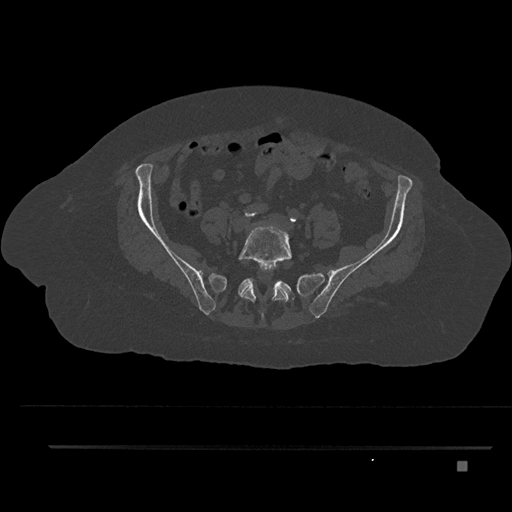
CT including the spine, one axial slice; slice 29 of 797 in the series (ordered by position); reconstruction kernel Br40s/3; 120 kVp; bone window (W 1800 / L 400 HU); 0.5 mm slice thickness; 512 × 512 image matrix, field of view 437 × 437 mm. Patient: female, 76 years. Case-level facts recorded for this patient, not image findings: primary cancer: lung.
Outlined on this slice (semi-automatic segmentation, software-assisted and operator-edited):
- L5 vertebra: bounding box <238,224,292,320> (left, top, right, bottom; pixels)